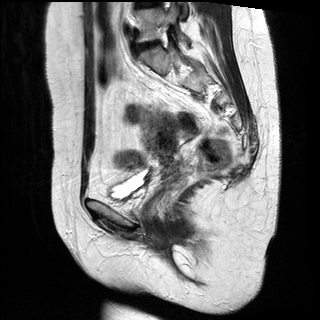
Pelvic MRI for cervical cancer, one sagittal slice; position 14 of 34 along the scan axis; T2-weighted; 1.5 T; TE 89 ms, TR 3320 ms; 320 × 320 image matrix, field of view 260 × 260 mm. Female patient, age 49 years.
Outlined on this slice (expert manual segmentation):
- uterus and cervix: bounding box <141,108,181,165> (left, top, right, bottom; pixels)